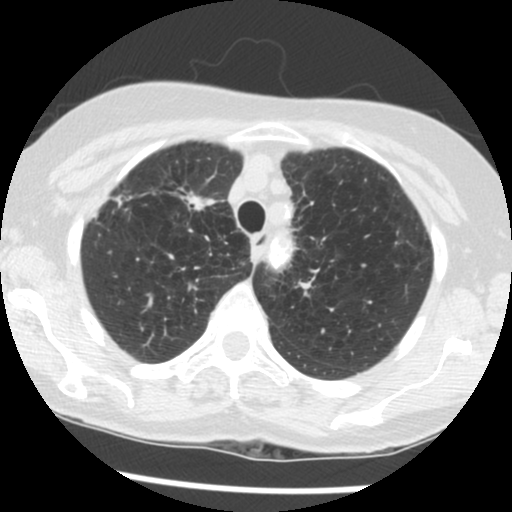
Low-dose screening chest CT, one axial slice; position 99 of 124 along the scan axis; 120 kVp; lung window (W 1500 / L -600 HU); 512 × 512 image matrix, field of view 290 × 290 mm.
Outlined on this slice (expert manual segmentation):
- lesion 1 (tumor, upper lobe of right lung): bounding box [x1, y1, x2, y2] px = [184, 192, 215, 210]